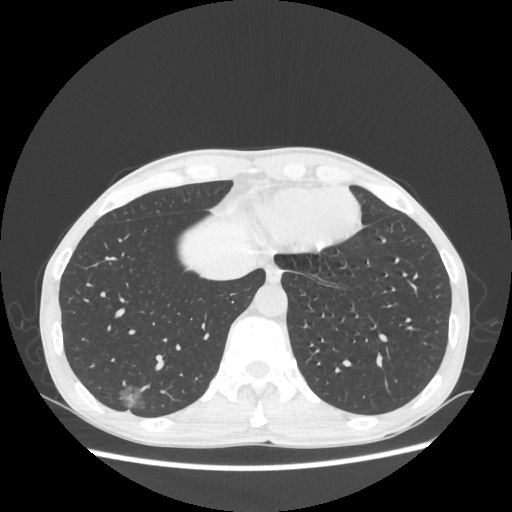
Chest CT, one axial slice. Slice 68 of 270 in the series (ordered by position). Reconstruction kernel STANDARD. 100 kVp. Lung window (W 1500 / L -600 HU). 512 × 512 image matrix. Male patient, age 60 years. From the clinical record (not read from this slice): clinical TNM (as recorded): T1c N0 M0.
Annotated regions visible in this slice (rectangle marked by the reading radiologist):
- lung tumour (recorded histology: adenocarcinoma): box from (x=110, y=382) to (x=151, y=424) px